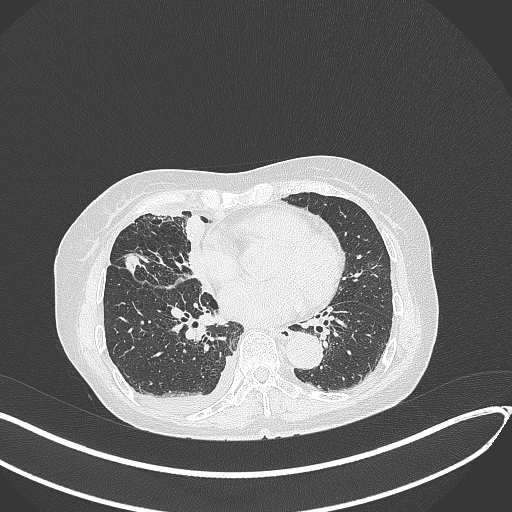
Chest CT, one axial slice. Slice 165 of 418 in the series (ordered by position). Reconstruction kernel B70f. Lung window (W 1500 / L -600 HU). 1 mm slice thickness. 512 × 512 image matrix. Female patient, age 75 years. From the clinical record (not read from this slice): clinical TNM (as recorded): T2a N3 M0.
Structures marked on this image (bounding box drawn by a radiologist):
- lung tumour (recorded histology: adenocarcinoma): bounding box (x1, y1, x2, y2) in pixels: (120, 251, 146, 280)